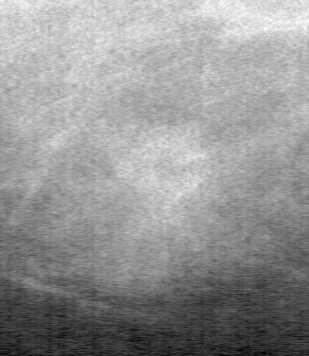
Region of interest cut from a scanned film mammogram (one marked finding); left breast; MLO view.
- Finding: mass, shape oval, margins ill defined; BI-RADS assessment category 4; subtlety rating 4 on a 1 (subtle) to 5 (obvious) scale; pathology (as recorded): benign.